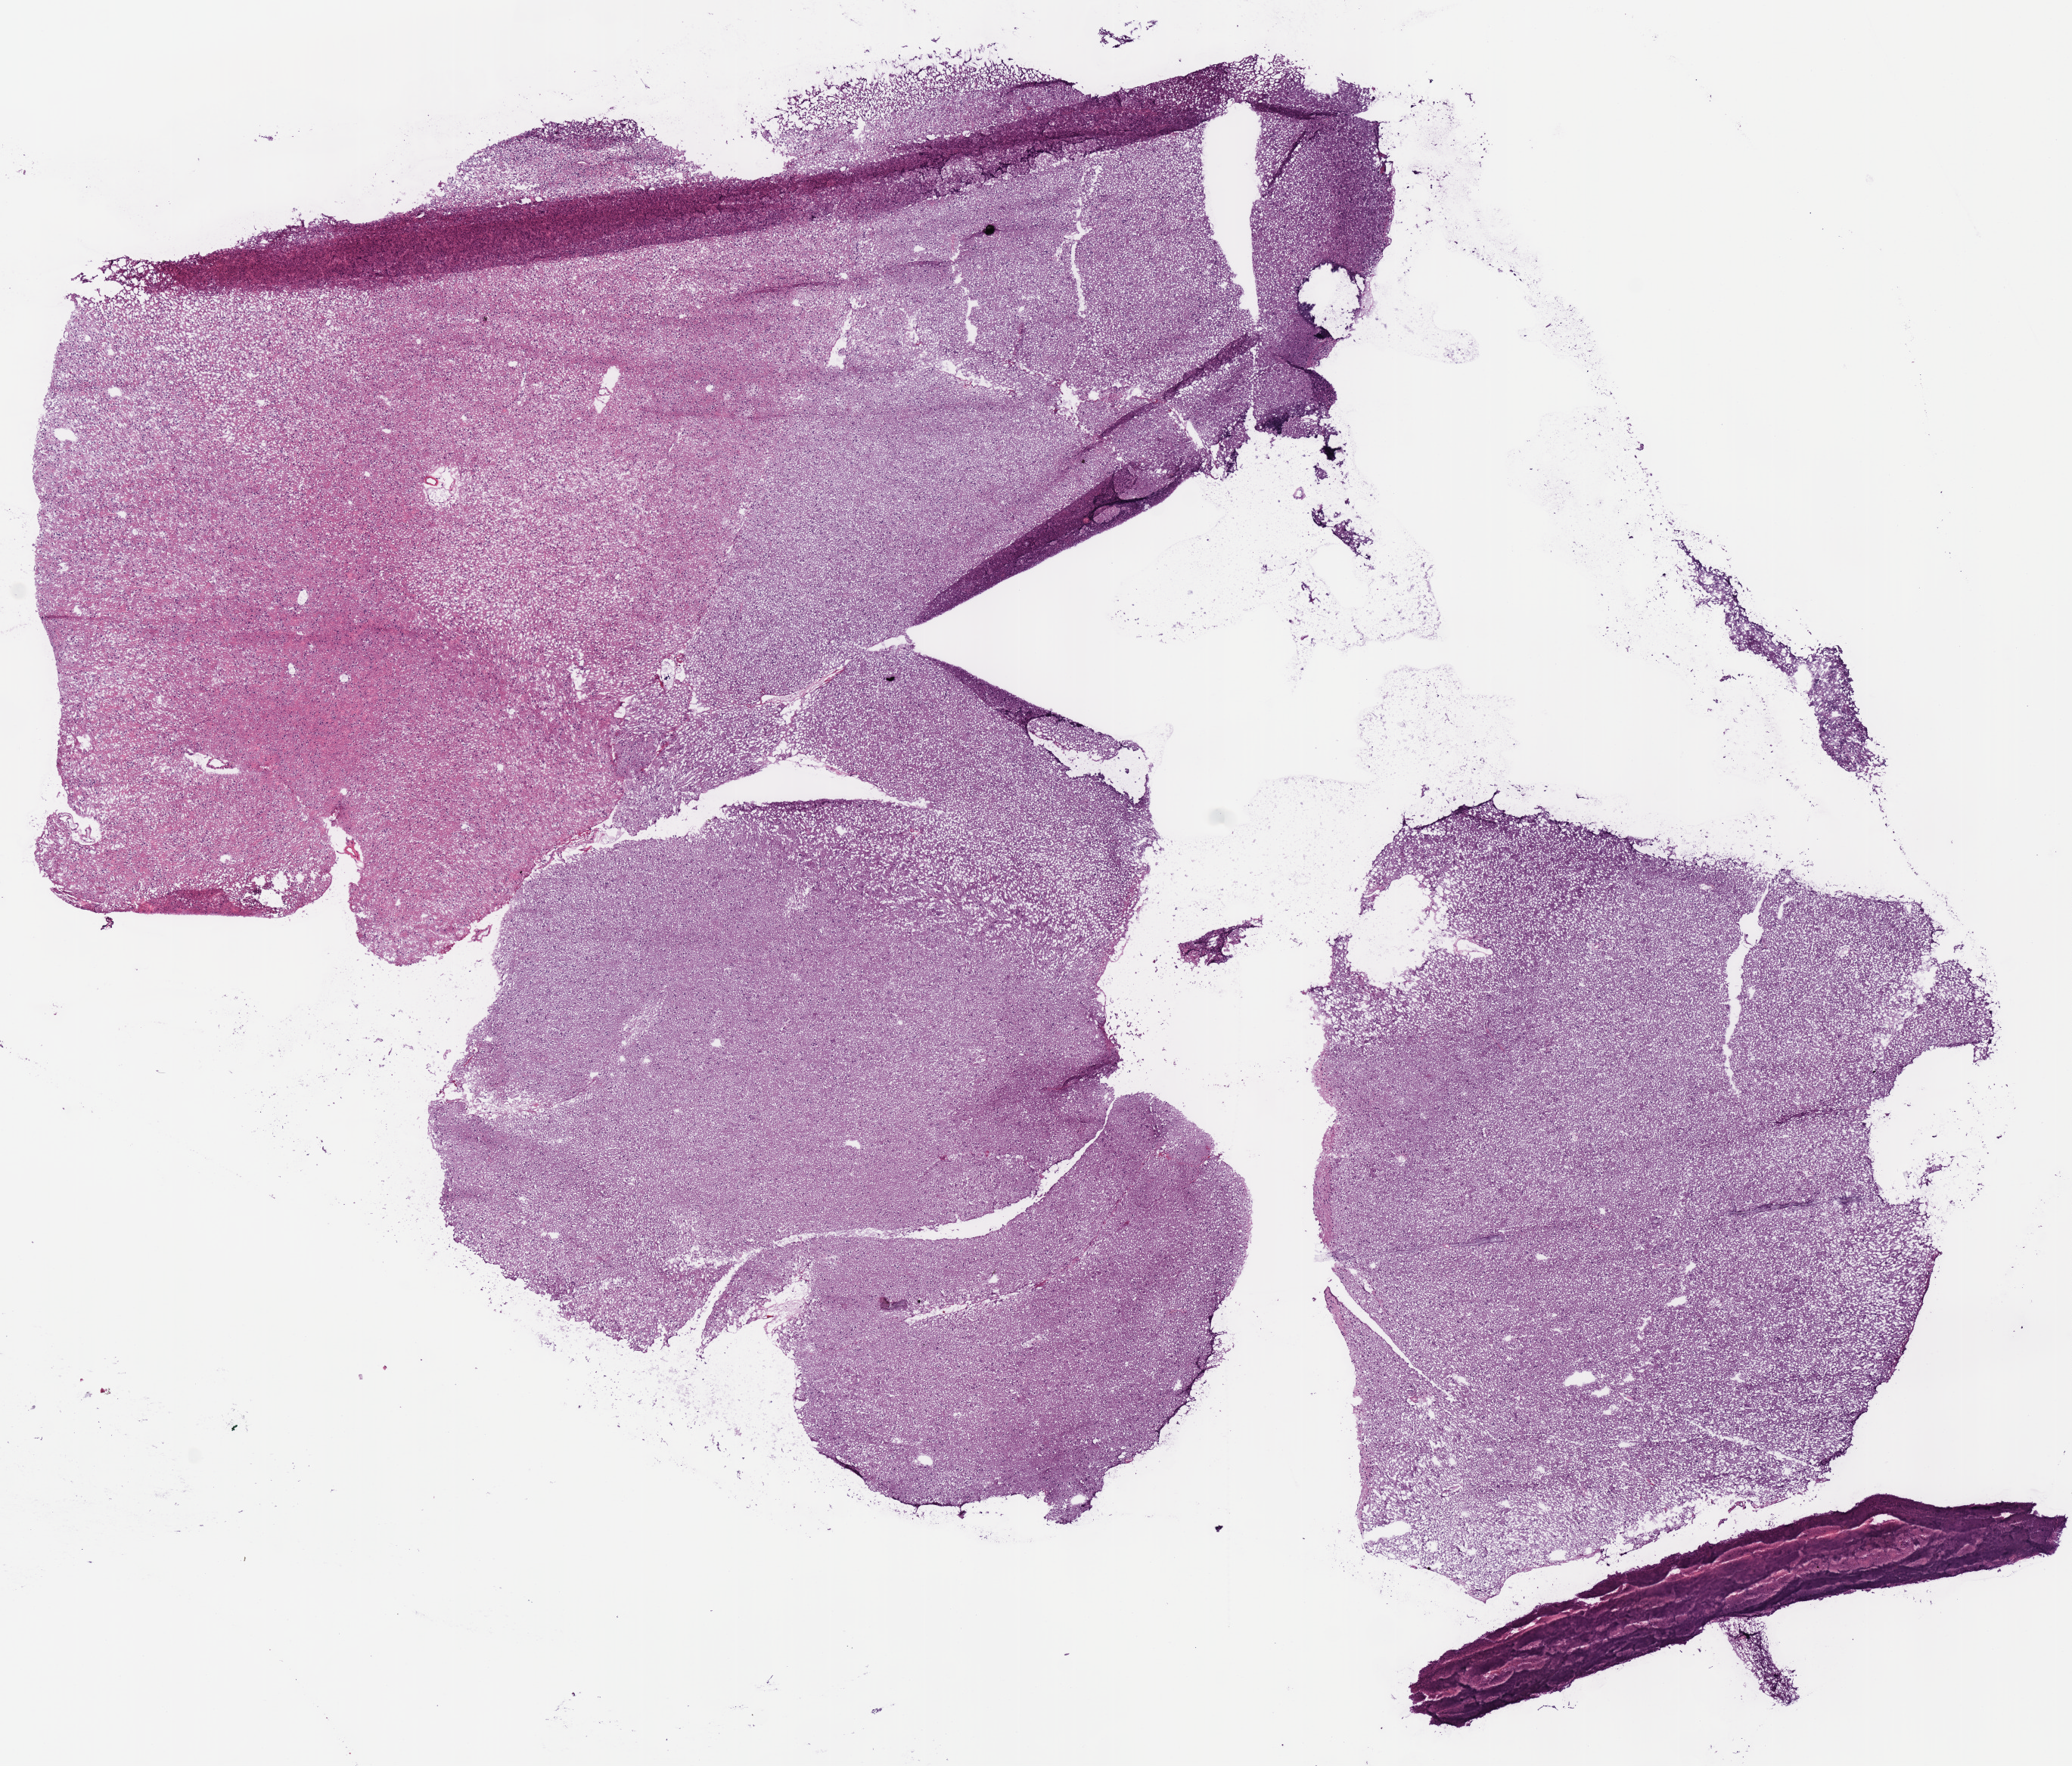
H&E-stained whole-slide image — low-resolution overview of the scanned area, about 10.8 x 9.2 mm (from a 40x scan); frozen section from the top of the tissue portion; brain, primary tumour sample. Female, age 29 years at initial diagnosis. Histologic grade: G2 (moderately differentiated). Pathologist review of this section (percent, as recorded): tumour cells 100%, tumour nuclei 60%, normal cells 0%, stromal cells 0%, necrosis 0%.
Pathologic diagnosis: Oligodendroglioma, NOS (cerebrum).